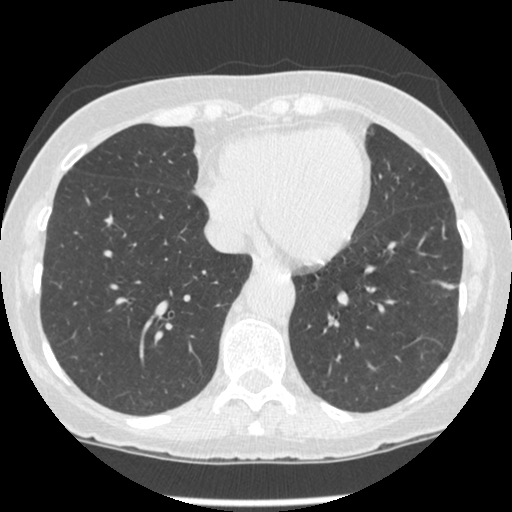
Low-dose screening chest CT, one axial slice. Slice 80 of 247 in the series (ordered by position). 120 kVp. Lung window (W 1500 / L -600 HU). 1.25 mm slice thickness. 512 × 512 image matrix.
Outlined on this slice (manually delineated by an expert):
- lesion 1 (tumor, lower lobe of left lung): box from (x=441, y=283) to (x=455, y=290) px